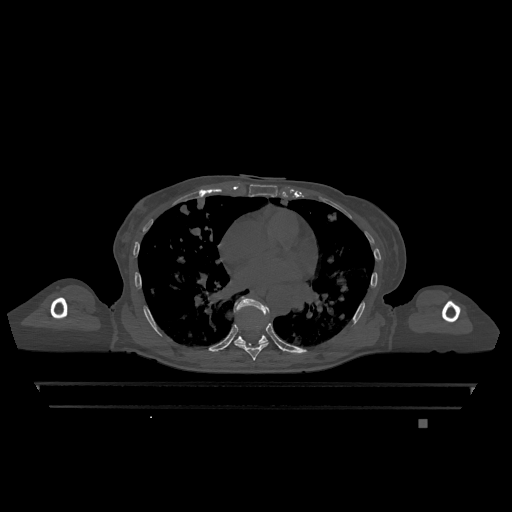
CT including the spine, one axial slice; slice 719 of 1317 in the series (ordered by position); bone window (W 1800 / L 400 HU); 0.5 mm slice thickness; 512 × 512 image matrix. Female patient, age 74 years. From the clinical record (not read from this slice): primary cancer: lung.
Outlined on this slice (semi-automatic segmentation, software-assisted and operator-edited):
- T7 vertebra: bounding box [x1, y1, x2, y2] px = [235, 343, 268, 361]
- T9 vertebra: [234, 297, 270, 345]